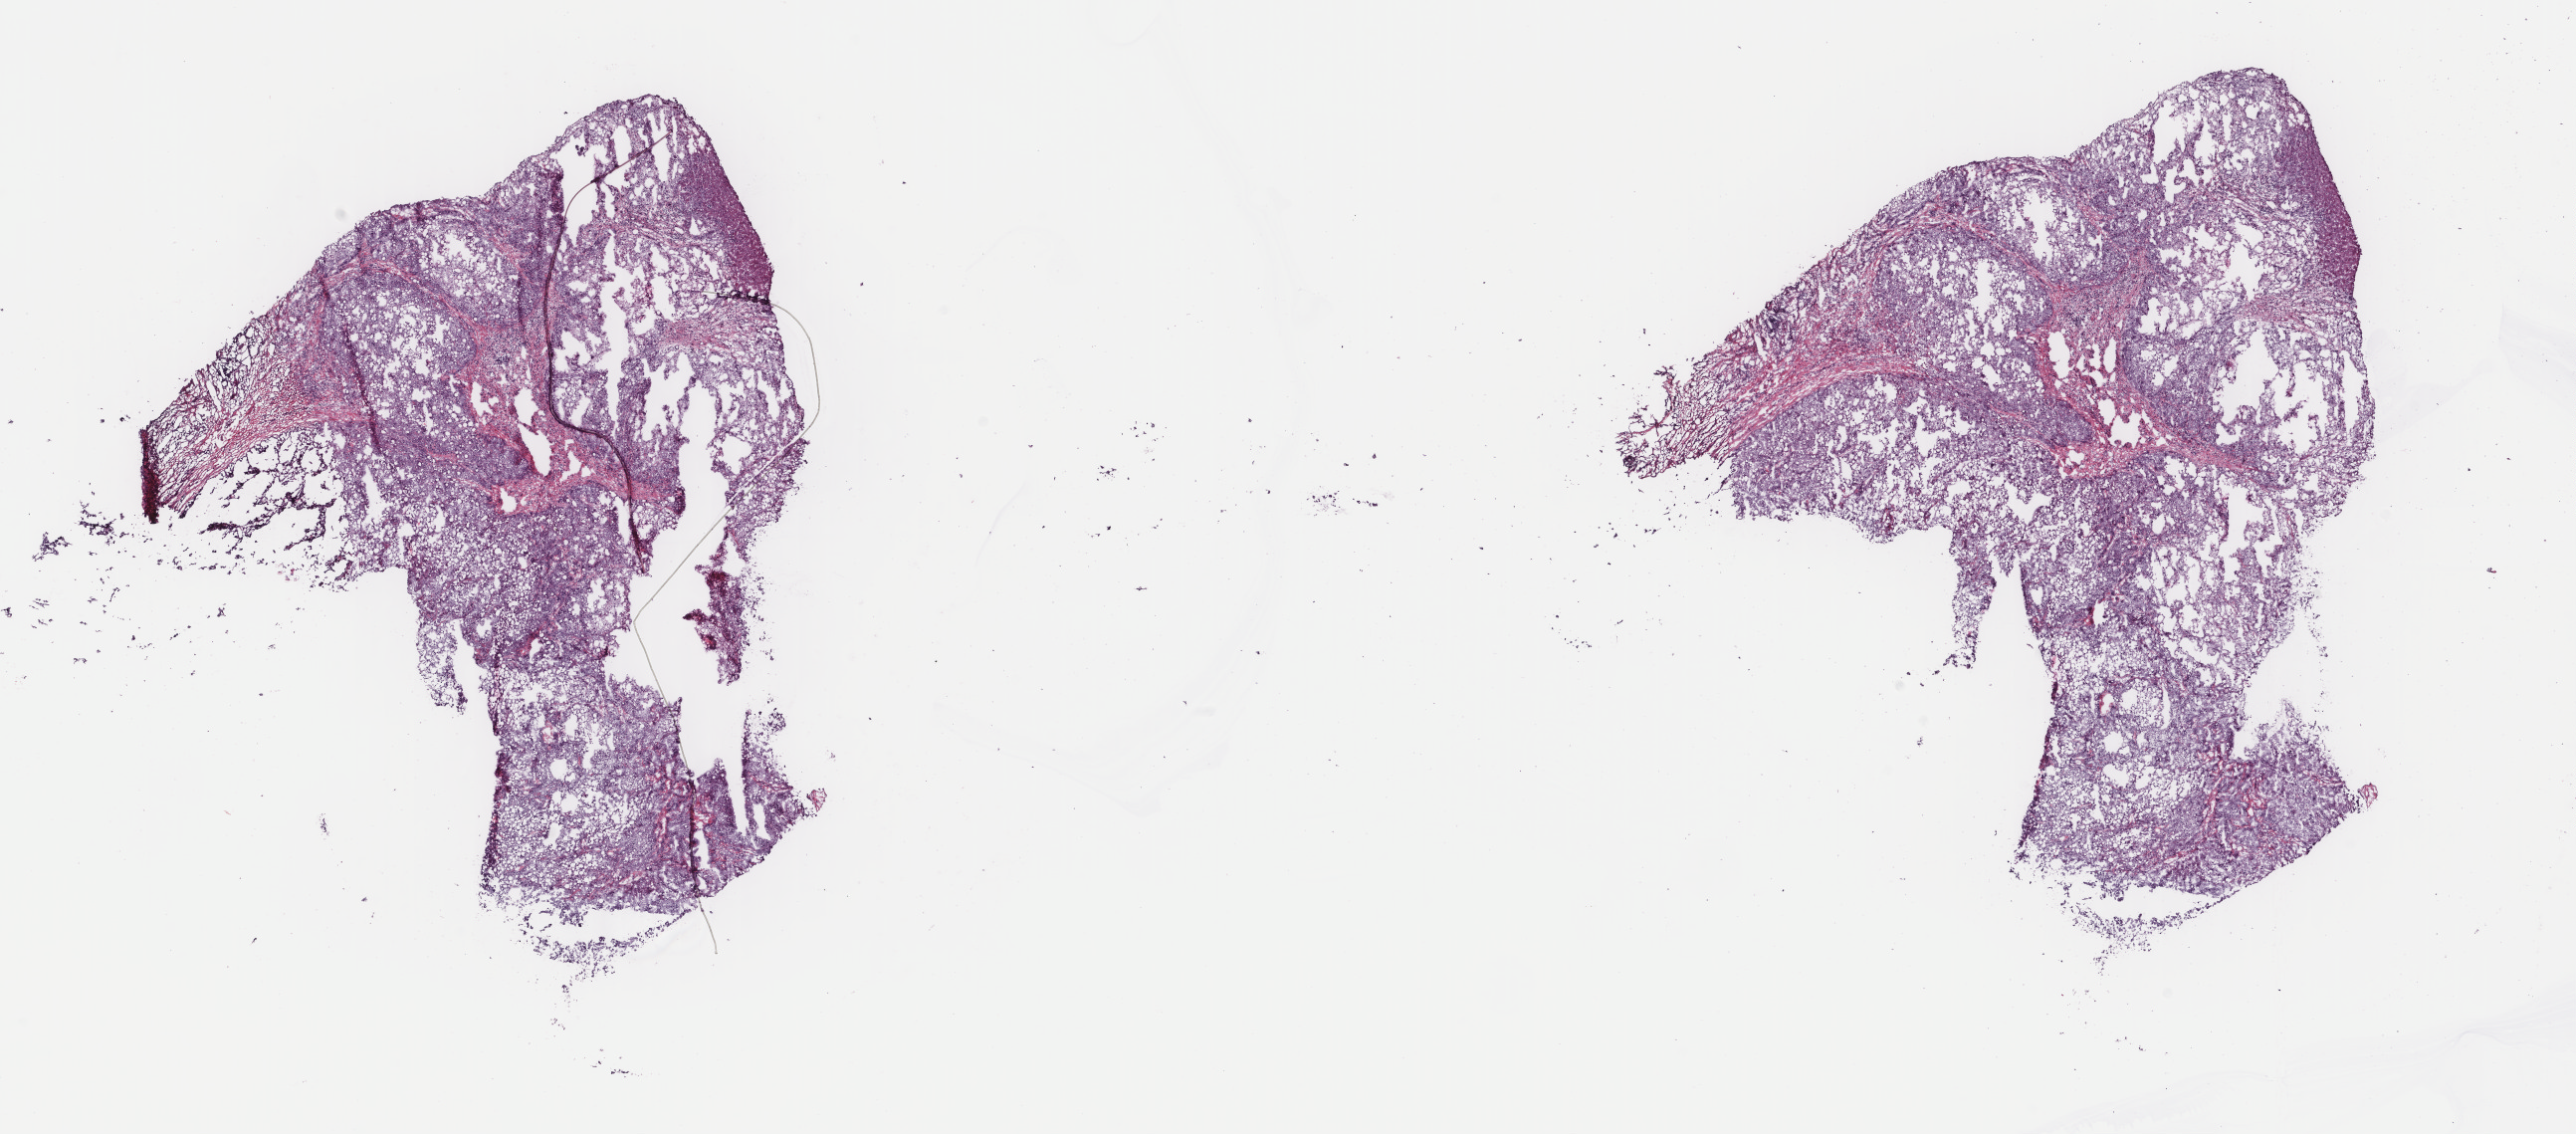
Hematoxylin and eosin (H&E) stained whole-slide image, a low-resolution overview of the entire scanned area, about 20.5 x 9.0 mm (from a 40x scan), frozen section from the top of the tissue portion, liver, primary tumour sample. Male patient; age at initial diagnosis 62 years. Histologic grade: G2 (moderately differentiated). Pathologist review of this section (percent, as recorded): tumour cells 100%, tumour nuclei 90%, normal cells 0%, stromal cells 0%, necrosis 0%. Infiltration values recorded for this section: lymphocyte infiltration 0%, monocyte infiltration 0%, neutrophil infiltration 0%.
Diagnosis: Hepatocellular carcinoma, NOS. AJCC pathologic stage: II (7th edition).